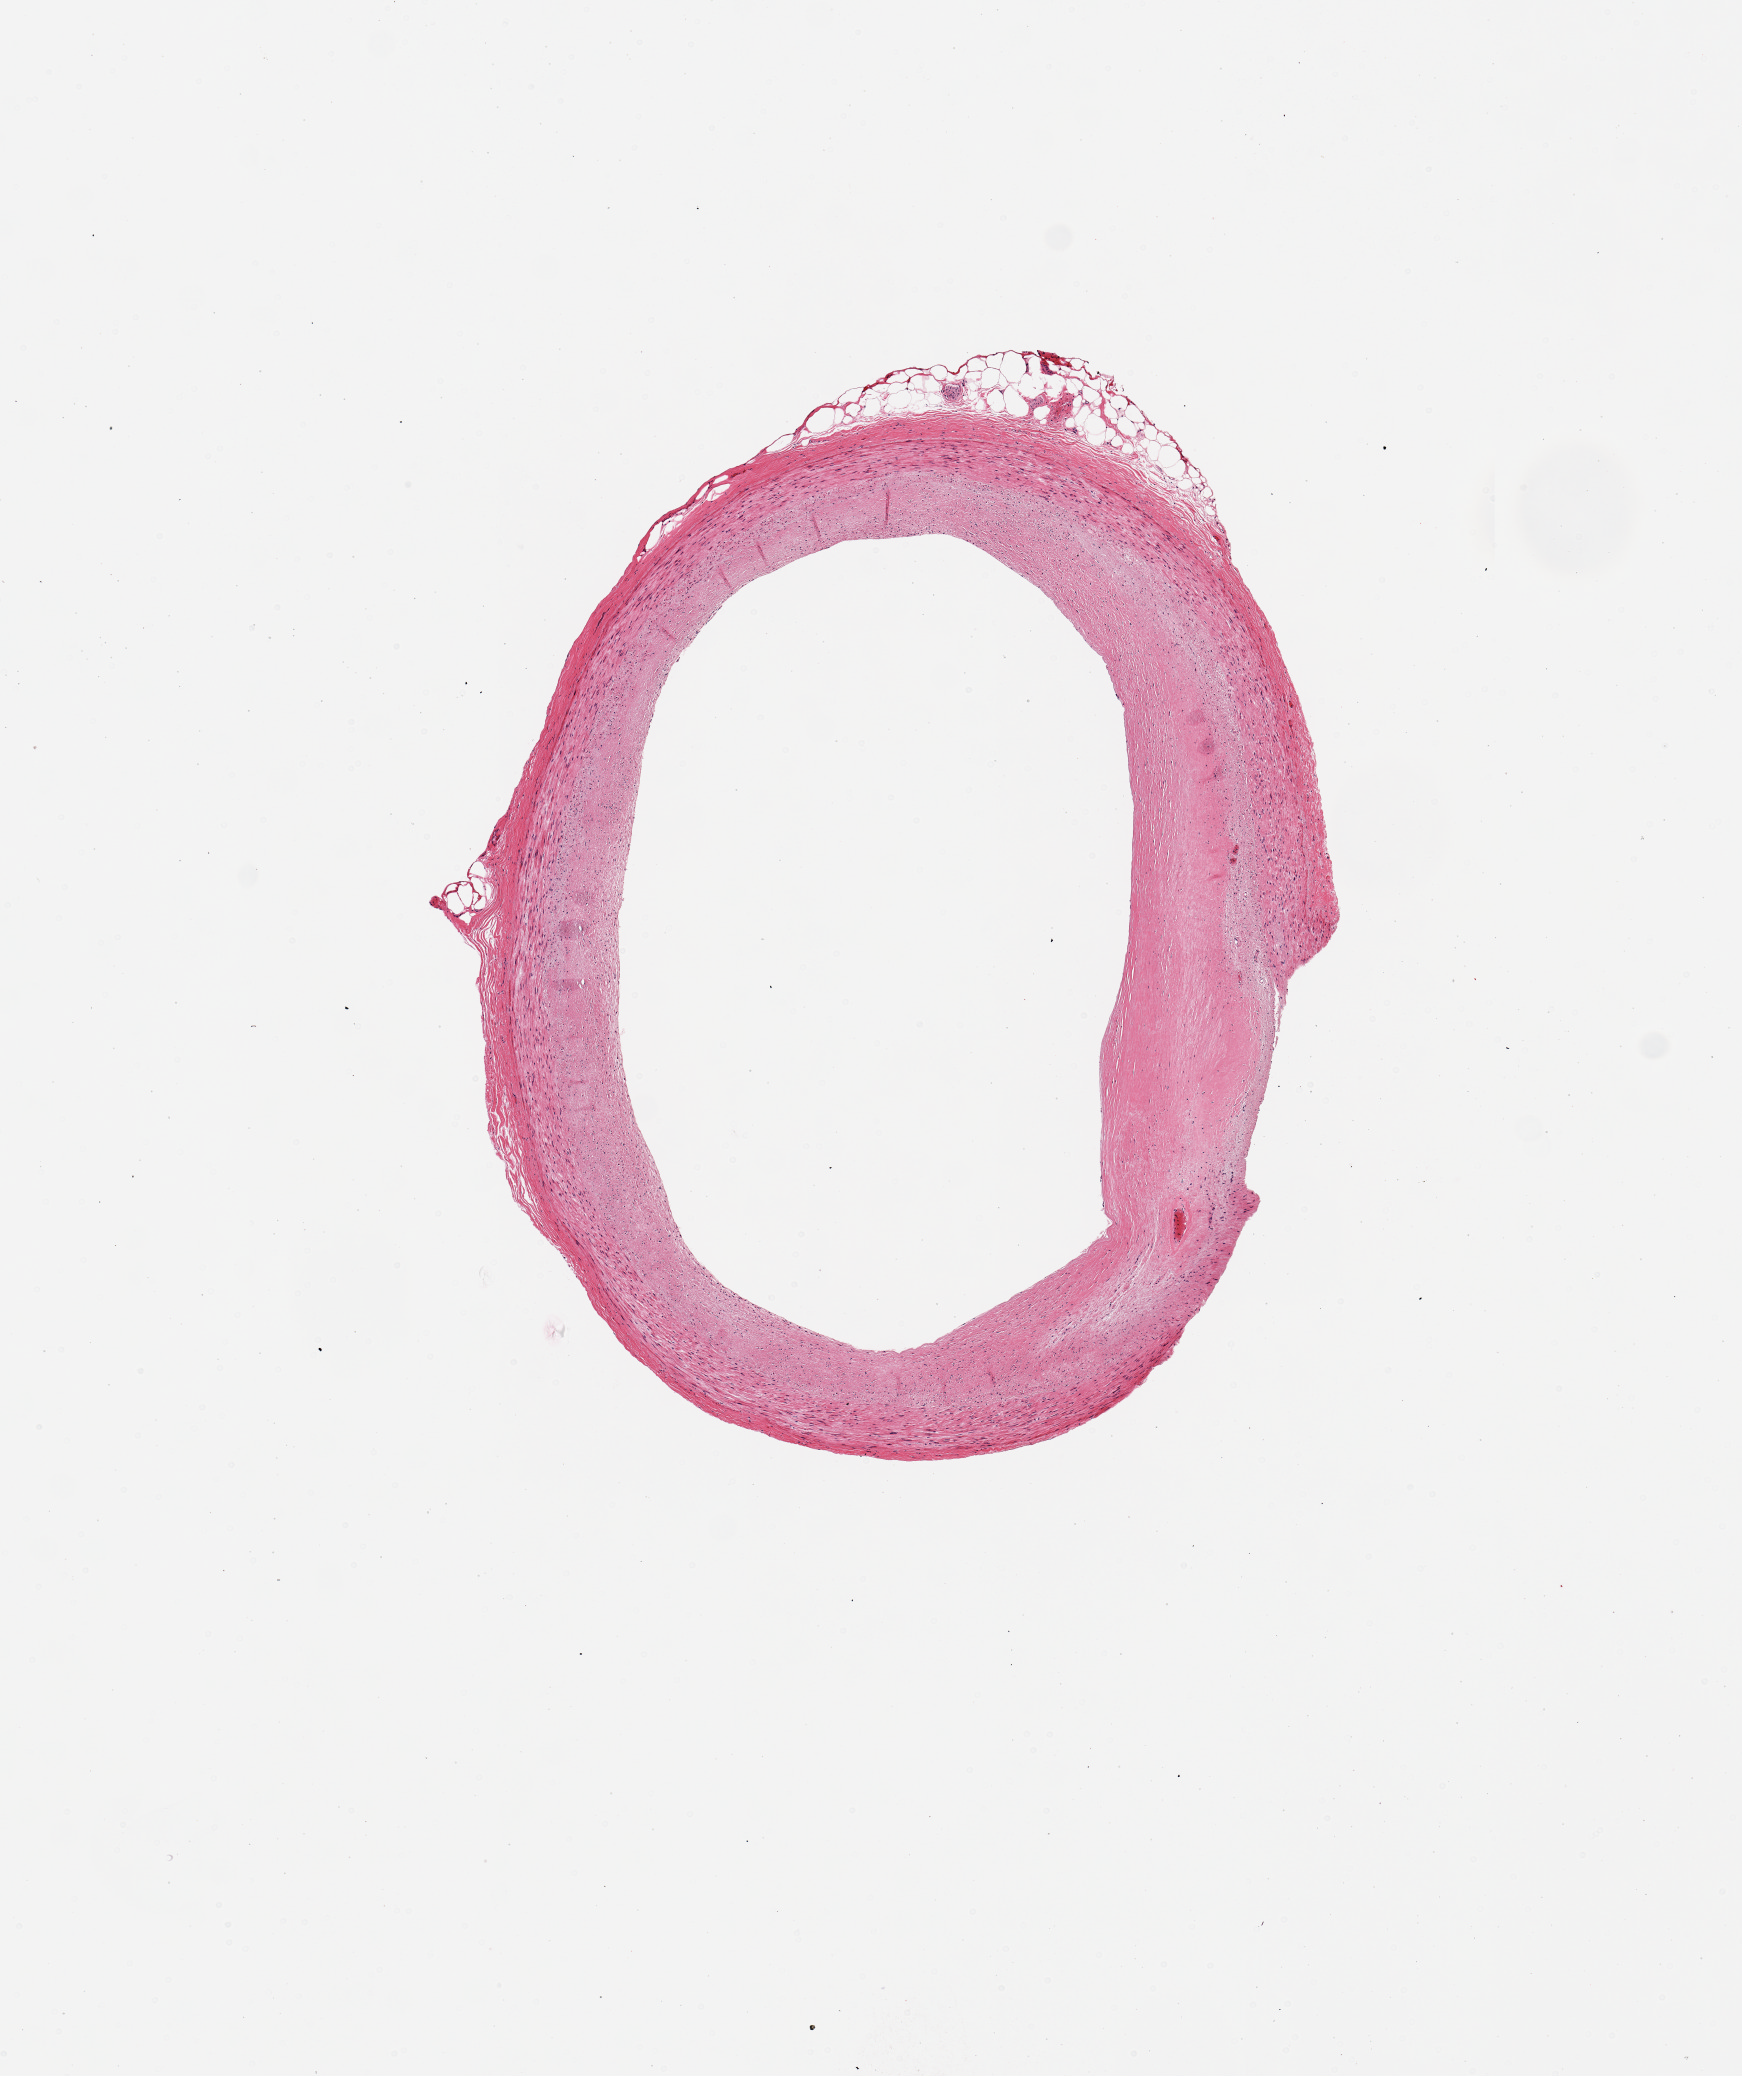
Digitized haematoxylin and eosin-stained section, brightfield, shown as a low-resolution overview of the whole scanned area (about 6.9 x 8.2 mm, slide scanned at 20x); PAXgene-fixed, paraffin-embedded tissue; sampled site (target tissue): coronary artery; donor tissue sample. Donor sex: male.
- review note (as recorded): 1 piece; atherosclerotic plaque; minimal external fat